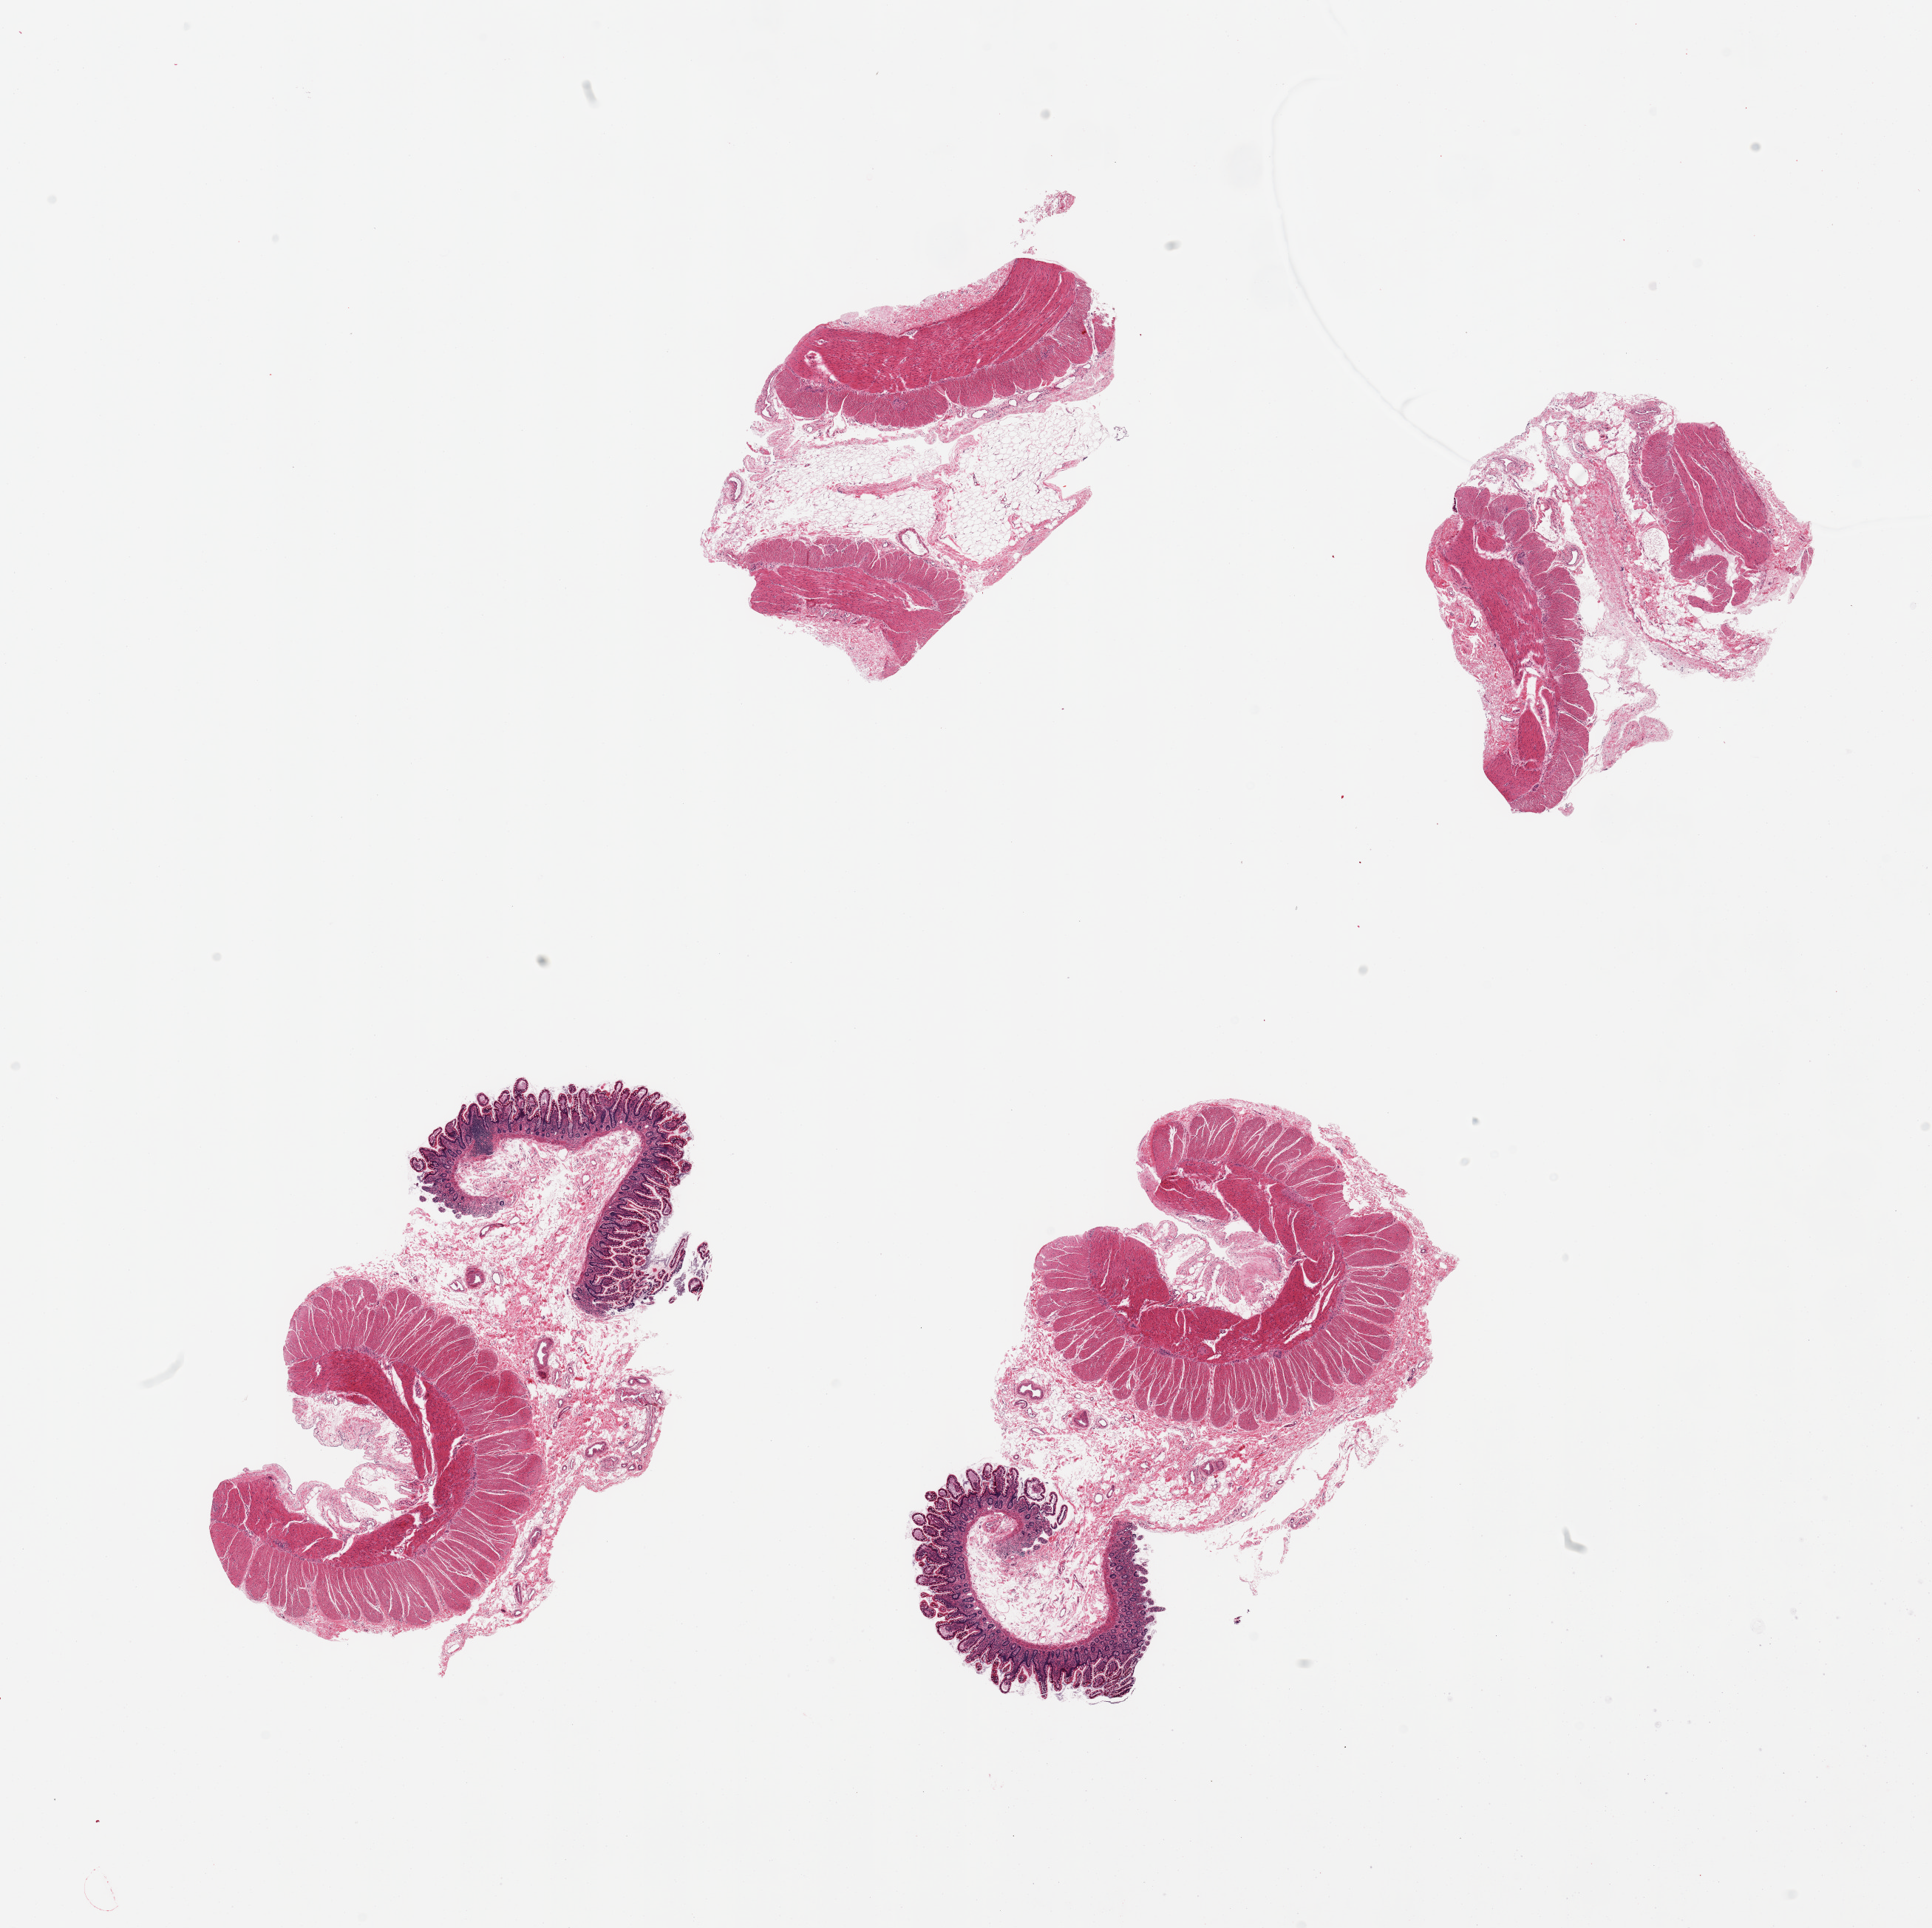
Digitized H&E-stained section, shown as a low-resolution overview of the whole scanned area (about 20.7 x 20.6 mm, from a 20x scan). PAXgene-fixed paraffin-embedded (PFPE) section. Sampled site (target tissue): ileum. Tissue donor sample. Female donor.
Reviewer comment on this tissue sample: 4 pieces, 2 with mucosa, well preserved but lymphoid aggregates insuffient to analyze.